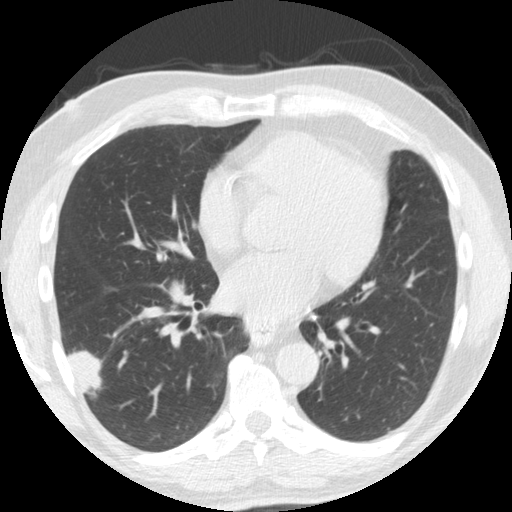
Axial slice from a low-dose chest CT screening exam; second screening round (one year after baseline); lung window (W 1500 / L -600 HU); 2.5 mm slice thickness; standard (soft-tissue) reconstruction kernel (STANDARD); slice 98 of 174 in the series; 512 × 512 image matrix. Male participant, aged 61 years at enrolment.
Expert-annotated lung lesion, box from (x=48, y=324) to (x=116, y=400) px. Reader record for this screening exam (exam-level; its link to the box is not recorded): non-calcified nodule or mass ≥4 mm, right lower lobe, 33 × 19 mm, smooth margins, soft tissue attenuation, pre-existing on the prior screen: yes; interval growth: yes. Participant outcome: lung cancer diagnosed 30 days after this screen — adenosquamous carcinoma, right lower lobe, poorly differentiated (G3), stage IV (AJCC 6th edition), 45 mm at pathology.